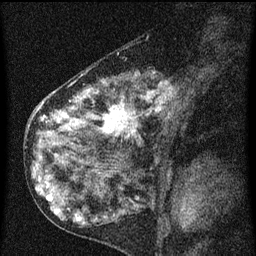
Breast MRI (dynamic contrast-enhanced), one sagittal slice. Dynamic contrast-enhanced series, image 2 of 3 at this slice position (ordered by acquisition). 1.5 T. TE 4.2 ms, TR 8 ms. 2 mm slice thickness. 256 × 256 image matrix, field of view 180 × 180 mm. Patient: female, 55 years.
Outlined on this slice (semi-automatic segmentation, software-assisted and operator-edited):
- analysis volume of interest (the breast-tissue region the enhancement analysis was run in; not a lesion): bounding box [x1, y1, x2, y2] px = [42, 72, 184, 155]
- tumour enhancement mask (voxels above the 70 % enhancement threshold inside the analysis volume of interest): [44, 82, 172, 139]